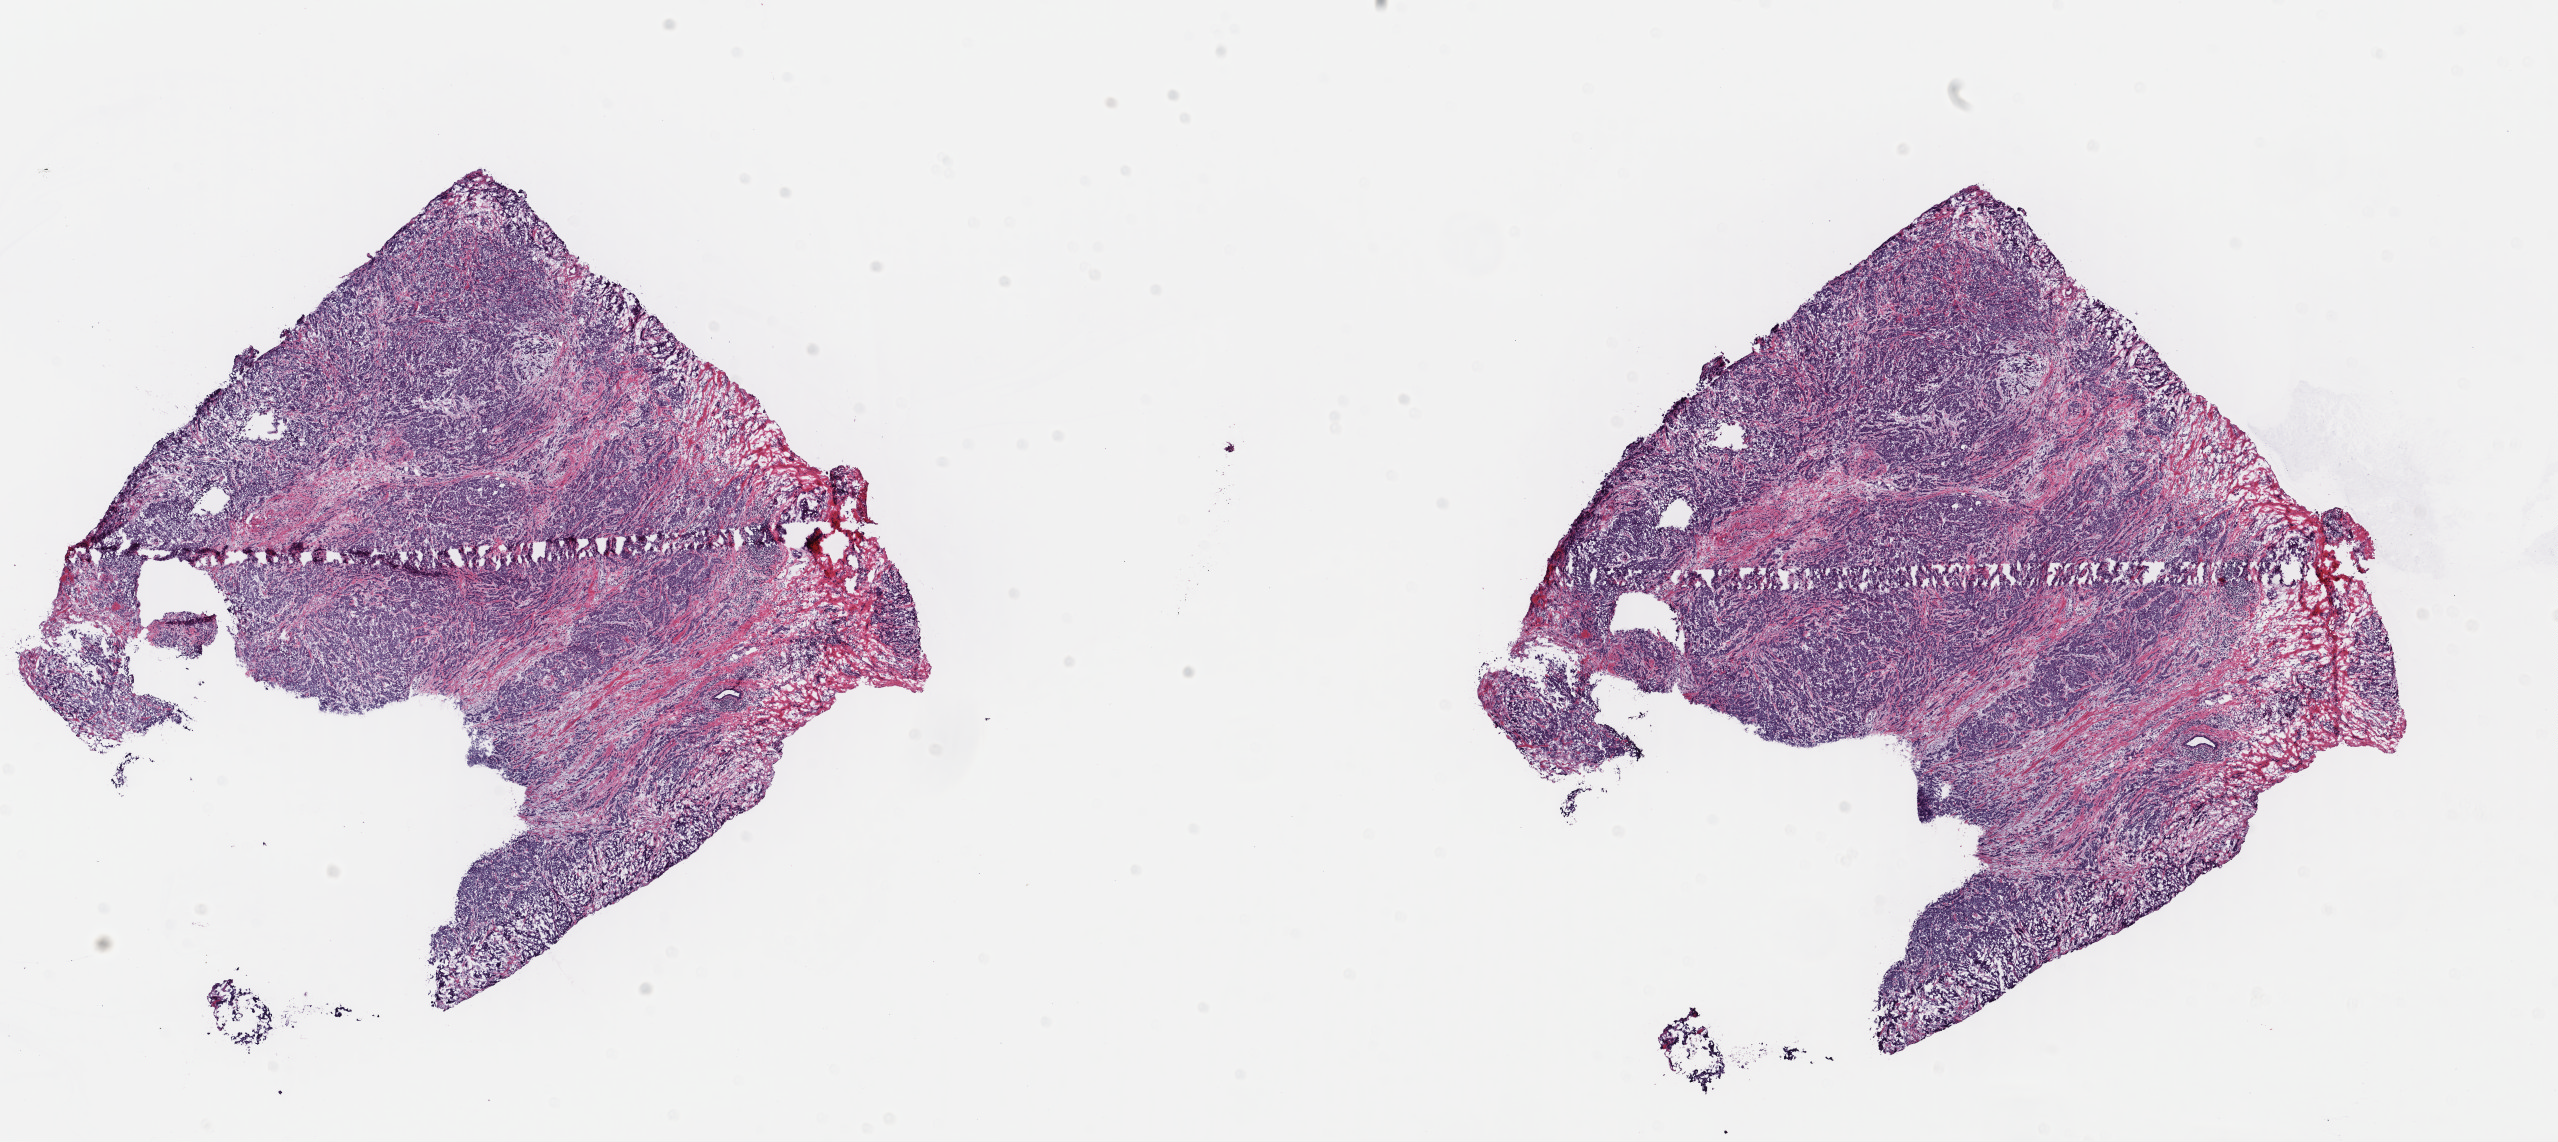
Digitized H&E tissue section (whole slide), a low-resolution overview of the entire scanned area, about 20.1 x 9.0 mm, frozen section from the top of the tissue portion, primary tumour sample from the breast. Female, age 61 years at initial diagnosis. Slide review estimates, as recorded: tumour cells 100%, tumour nuclei 90%, normal cells 0%, stromal cells 0%, necrosis 0%. Infiltration values recorded for this section: lymphocyte infiltration 0%, monocyte infiltration 0%, neutrophil infiltration 0%.
• diagnosis: Infiltrating duct carcinoma, NOS
• lymph nodes positive (case pathology): 5 of 8 examined
• AJCC pathologic stage: IIIA (7th edition)